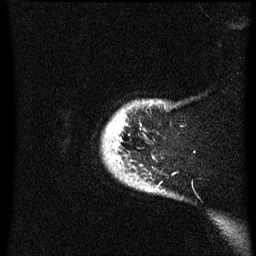
Breast MRI (dynamic contrast-enhanced), one sagittal slice. Position 56 of 60 along the scan axis. Dynamic contrast-enhanced series, image 2 of 3 at this slice position (ordered by acquisition). 1.5 T. TE 4.2 ms, TR 8.4 ms. 2.3 mm slice thickness. 256 × 256 image matrix, field of view 200 × 200 mm. Female patient, age 38 years. Case-level facts recorded for this patient, not image findings: setting: breast cancer imaged before/during neoadjuvant chemotherapy; receptor status: HER2-positive.
Outlined on this slice (semi-automatic segmentation, software-assisted and operator-edited):
- analysis volume of interest (the breast-tissue region the enhancement analysis was run in; not a lesion): box from (x=102, y=100) to (x=179, y=197) px
- tumour enhancement mask (voxels above the 70 % enhancement threshold inside the analysis volume of interest): (x=109, y=116)–(x=125, y=159)